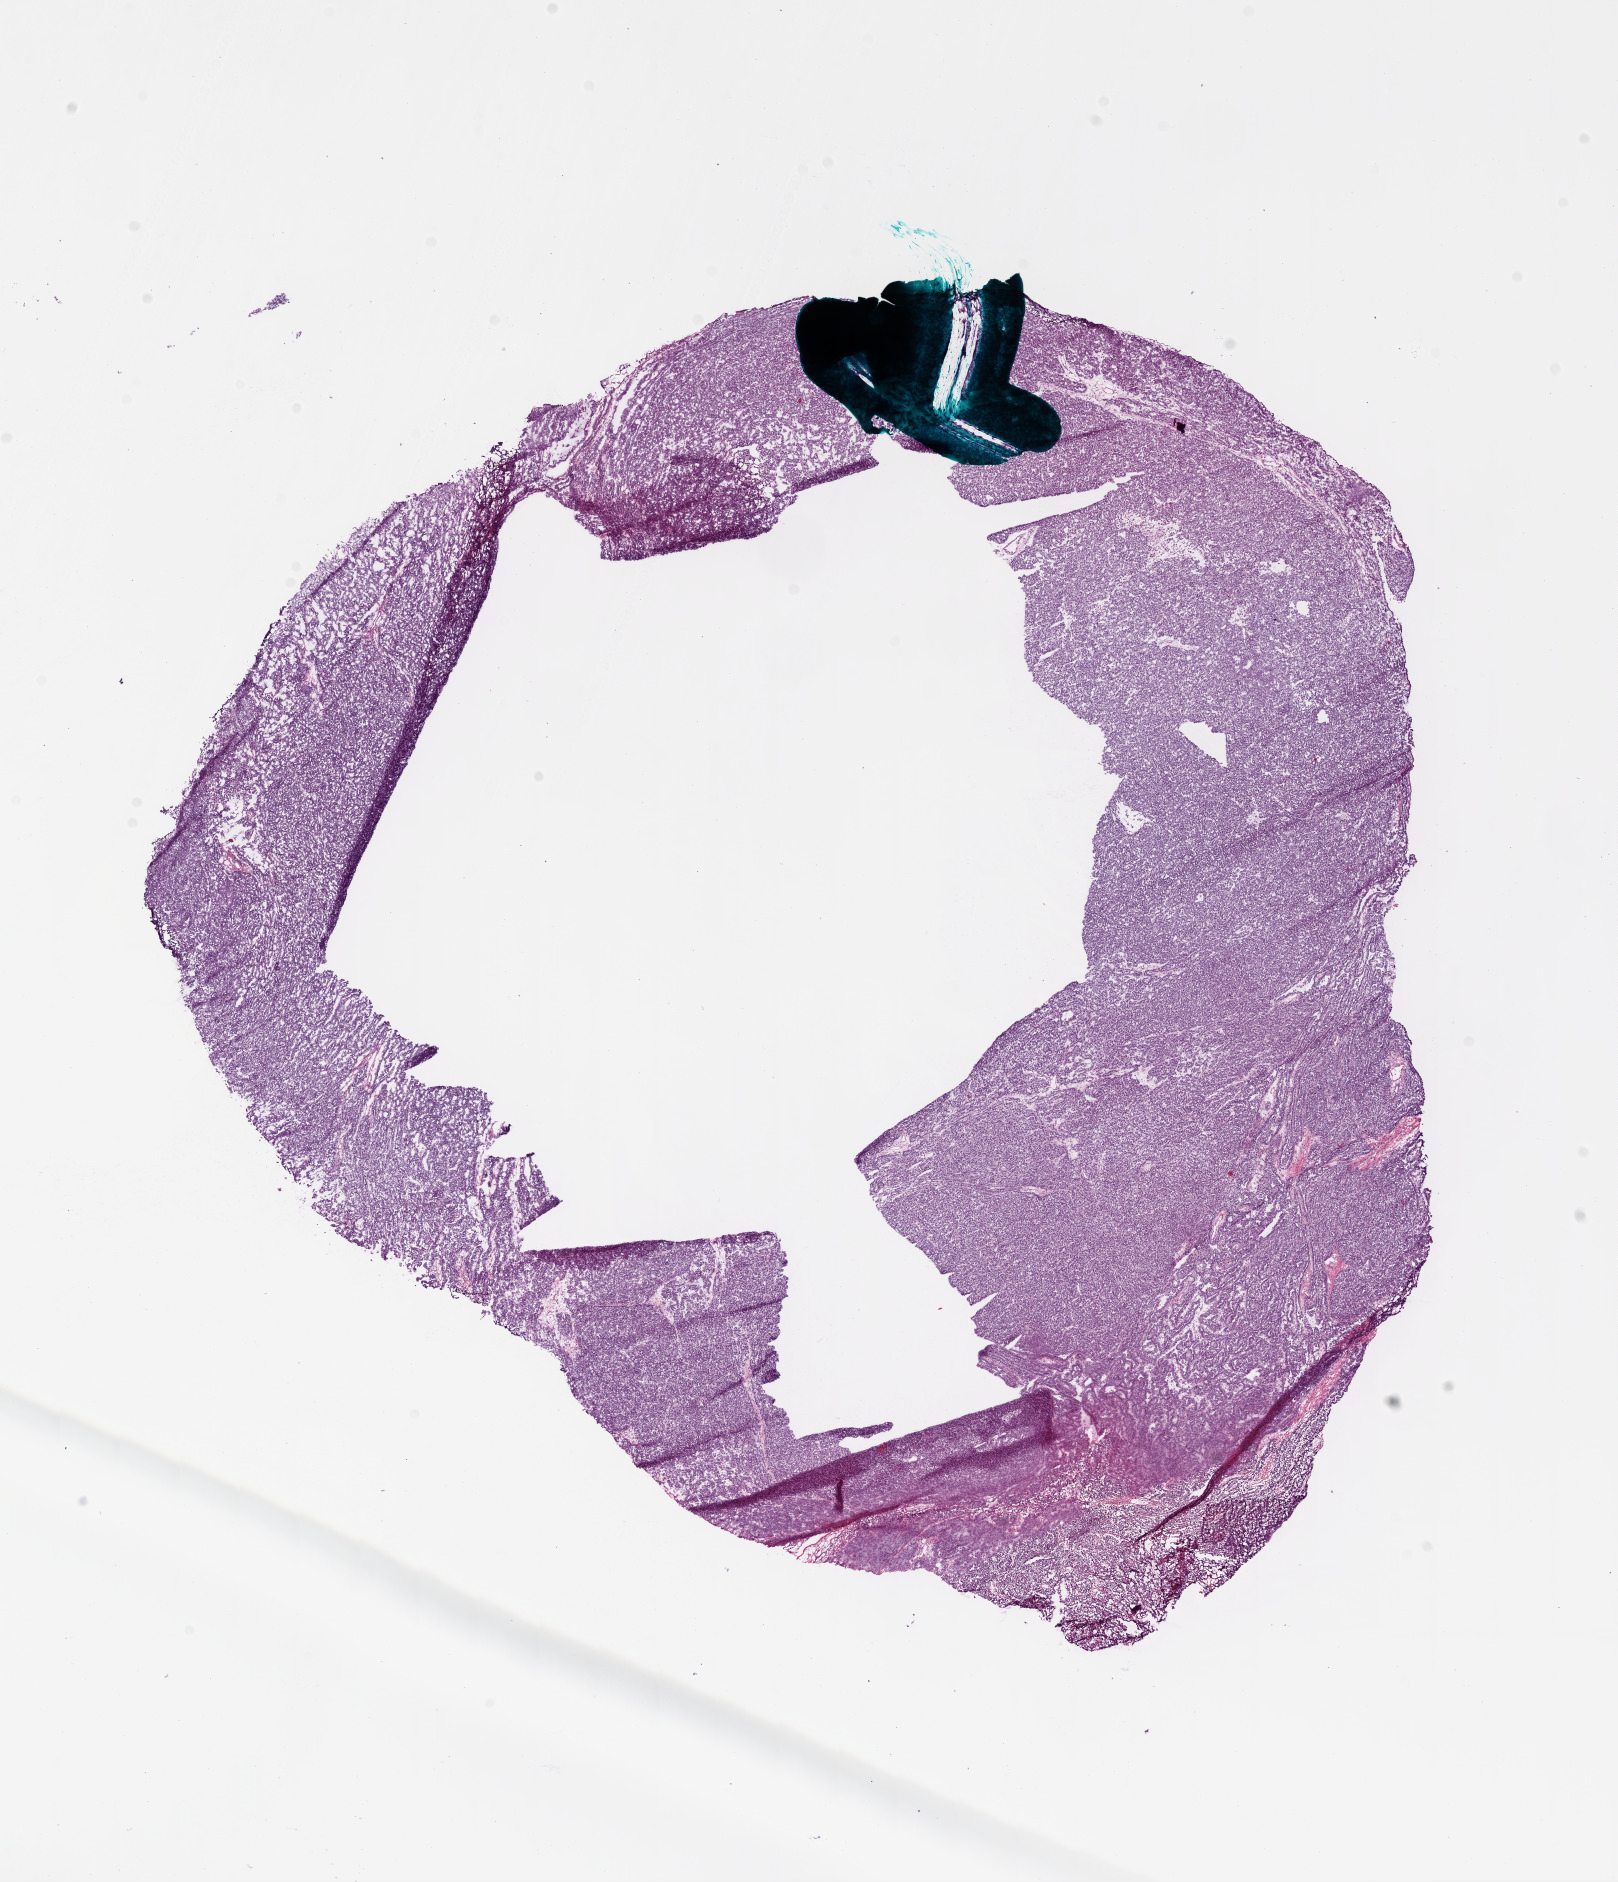
Digitized H&E-stained tissue section (whole slide), a low-resolution overview of the entire scanned area, about 13.1 x 15.2 mm (from a 20x scan), frozen section from the bottom of the tissue portion, ovary, primary tumour sample. Patient: female, age at initial diagnosis 74 years. Histologic grade: G3 (poorly differentiated). Slide review estimates, as recorded: tumour cells 78%, tumour nuclei 80%, normal cells 18%, stromal cells 2%, necrosis 2%.
FIGO stage: IIIC. Diagnosis: Serous cystadenocarcinoma, NOS.